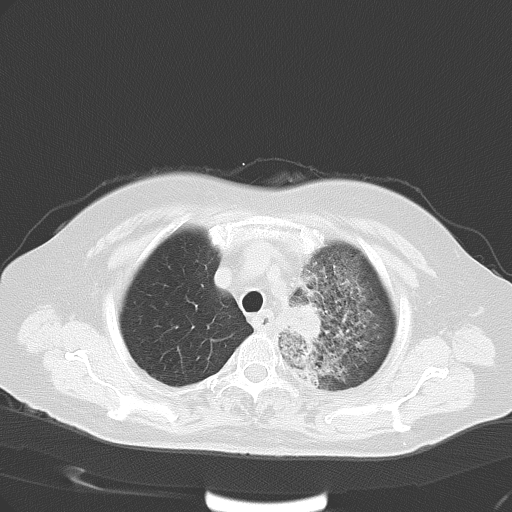
Chest CT, one axial slice. Position 45 of 54 along the scan axis. Reconstruction kernel B70f. 120 kVp. Lung window (W 1500 / L -600 HU). 5 mm slice thickness. 512 × 512 image matrix, field of view 353 × 353 mm. Female patient, age 65 years. From the clinical record (not read from this slice): clinical TNM (as recorded): T2b N1 M0.
Outlined on this slice (bounding box drawn by a radiologist):
- lung tumour (recorded histology: adenocarcinoma): bounding box [x1, y1, x2, y2] px = [288, 300, 322, 349]